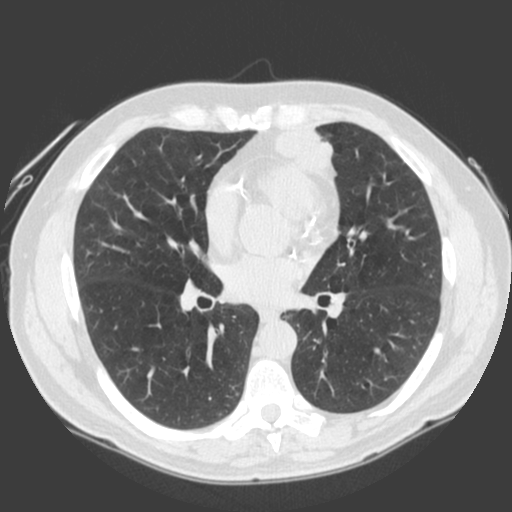
Low-dose screening chest CT, one axial slice; lung window (W 1500 / L -600 HU); 512 × 512 image matrix, field of view 360 × 360 mm.
Annotated regions visible in this slice (expert manual segmentation):
- lesion 1 (tumor, lower lobe of left lung): bounding box (x1, y1, x2, y2) in pixels: (274, 124, 333, 173)